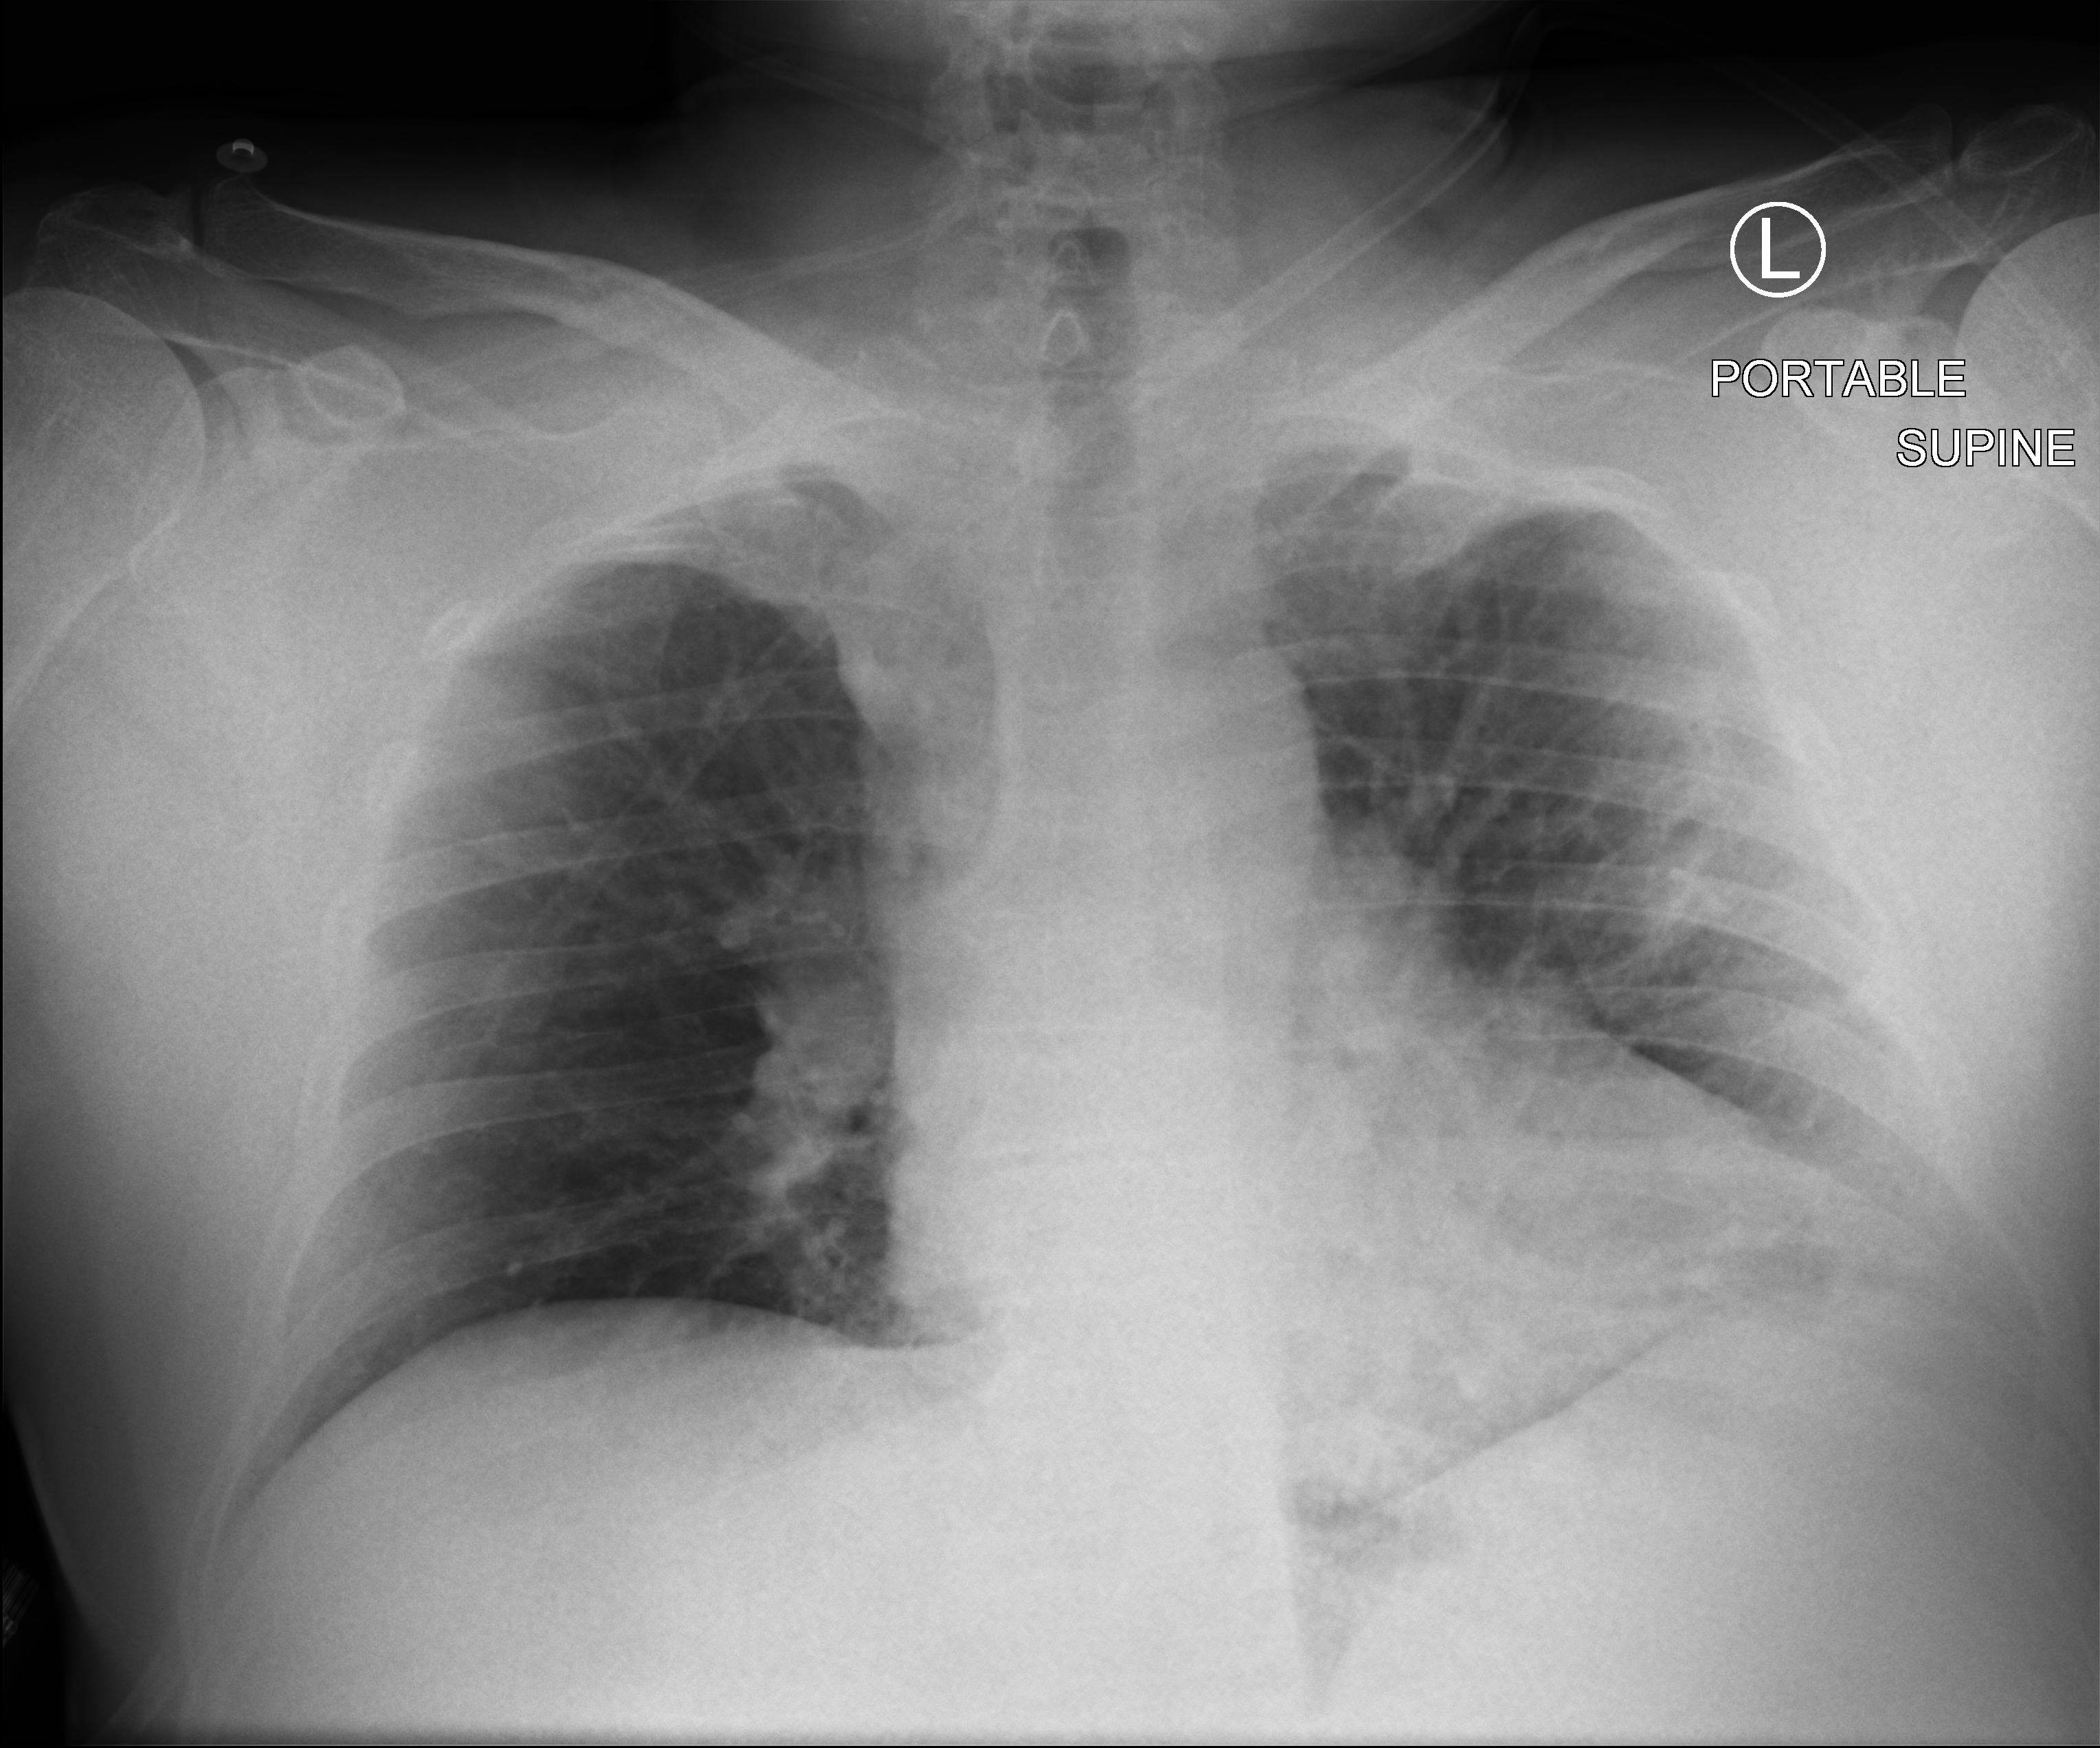
Chest X-ray (portable), anteroposterior (AP) projection. Patient hospitalised with COVID-19; male, aged 60–74 years.
From the hospital-stay record, not from the radiograph (when in the stay this image was taken is not recorded): mechanically ventilated during this hospital stay: no; hypertension (admission record): no; admitted to intensive care during this hospital stay: no.